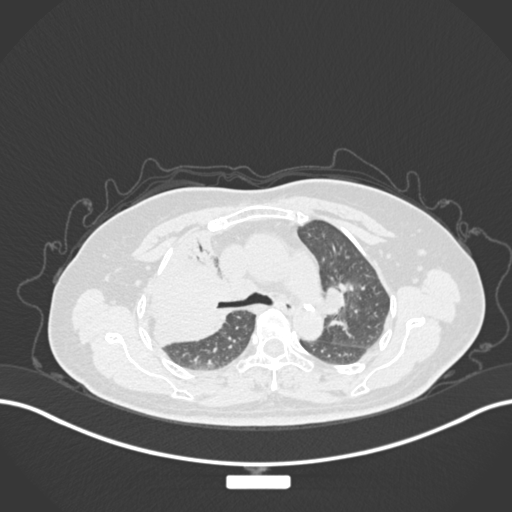
Chest CT, one axial slice; slice 105 of 177 in the series (ordered by position); 120 kVp; lung window (W 1500 / L -600 HU); 1 mm slice thickness; 512 × 512 image matrix. Patient: female, 60 years. From the clinical record (not read from this slice): clinical TNM (as recorded): T3 N1 M1.
Annotated regions visible in this slice (rectangle marked by the reading radiologist):
- lung tumour (recorded histology: adenocarcinoma): bounding box <150,232,233,352> (left, top, right, bottom; pixels)